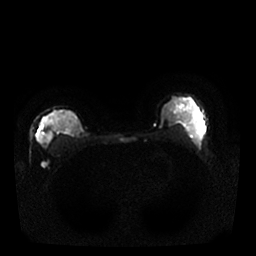
Breast MRI, one axial slice; slice 17 of 25 in the series (ordered by position); diffusion-weighted series; image 2 of 4 stored at this slice position (different b-values; order by instance number); 1.5 T; 4 mm slice thickness; 256 × 256 image matrix. Female patient.
Annotated regions visible in this slice (expert manual segmentation):
- tumour on diffusion-weighted imaging: bounding box <38,123,45,137> (left, top, right, bottom; pixels)